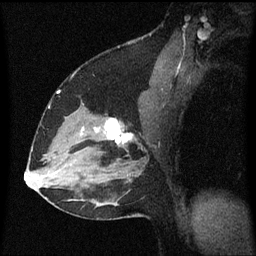
Breast MRI (dynamic contrast-enhanced), one sagittal slice. Dynamic contrast-enhanced series, image 2 of 3 at this slice position (ordered by acquisition). 1.5 T. TE 4.2 ms, TR 8.4 ms. 256 × 256 image matrix, field of view 200 × 200 mm. Patient: female, 37 years. From the clinical record (not read from this slice): setting: breast cancer imaged before/during neoadjuvant chemotherapy; receptor status: HR-positive, HER2-negative.
Structures marked on this image (semi-automatic segmentation, software-assisted and operator-edited):
- analysis volume of interest (the breast-tissue region the enhancement analysis was run in; not a lesion): bounding box [x1, y1, x2, y2] px = [94, 114, 141, 157]
- tumour enhancement mask (voxels above the 70 % enhancement threshold inside the analysis volume of interest): [95, 118, 133, 145]